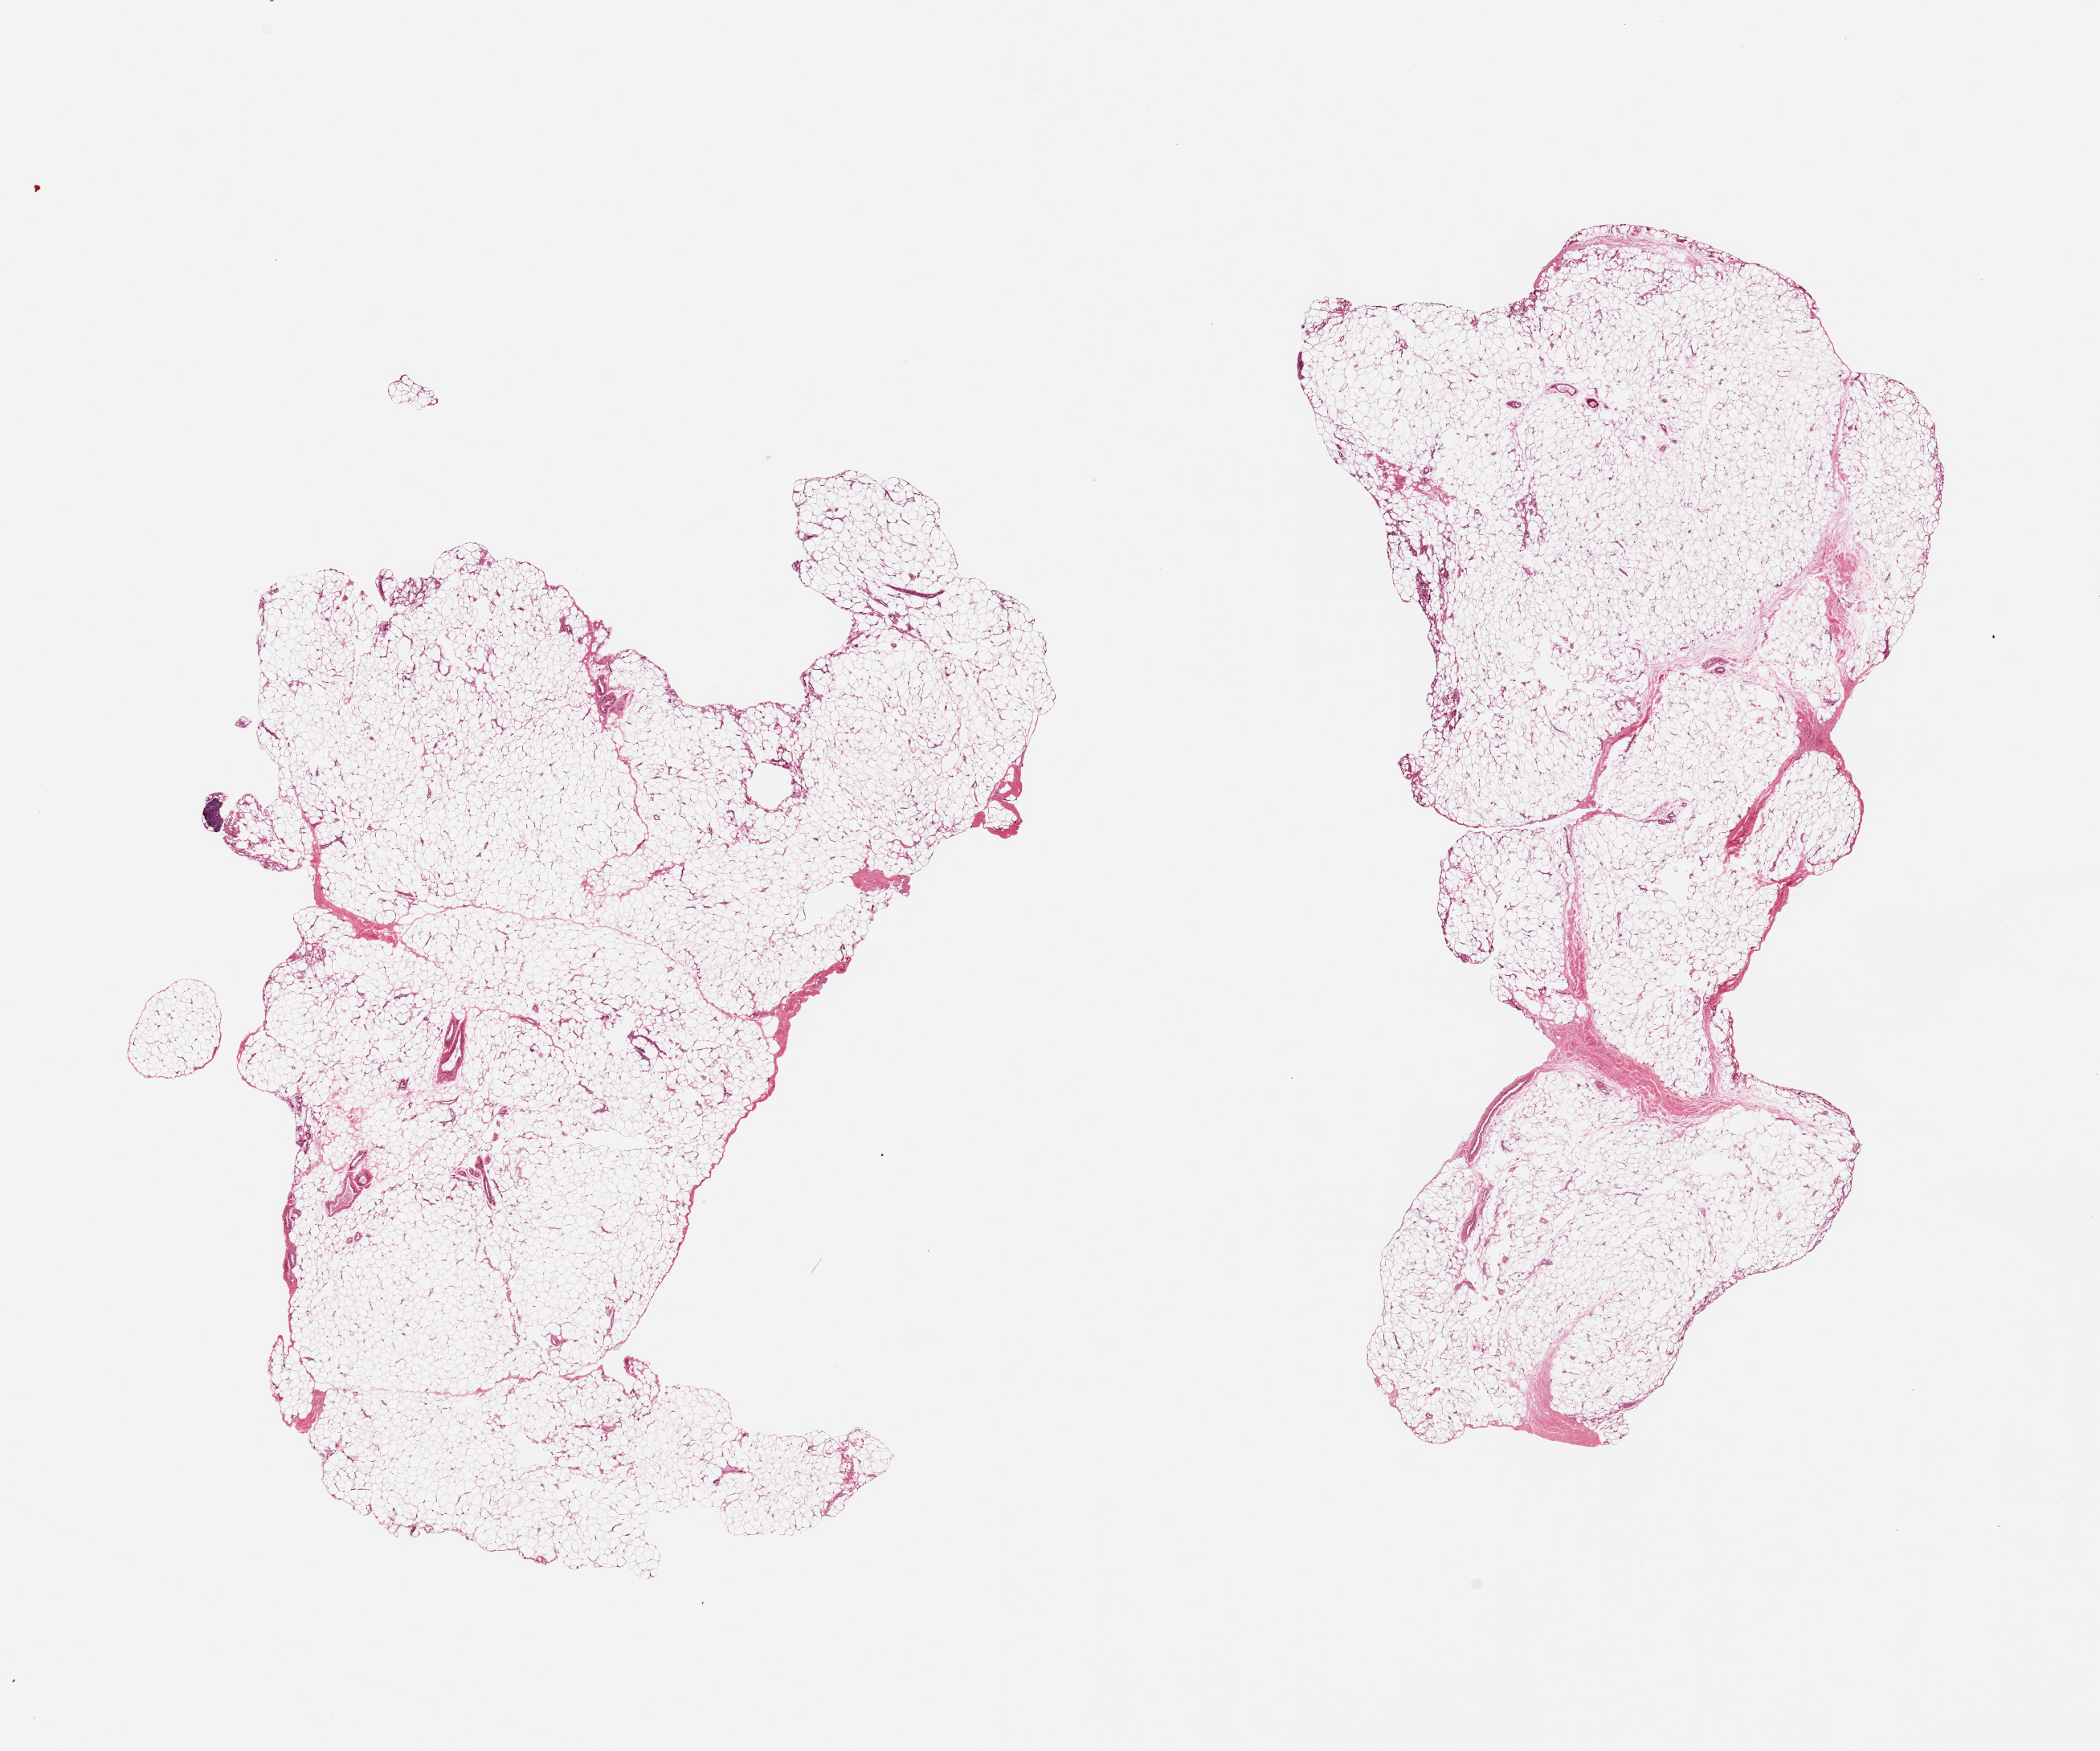
Whole-slide image, hematoxylin and eosin (H&E) stain, brightfield, a low-resolution overview of the entire scanned area, about 20.7 x 17.2 mm (from a 20x scan), PAXgene-fixed, paraffin-embedded tissue, section of adipose tissue (target tissue), donor tissue sample. Female donor.
* review note (as recorded): 2 pieces; small squamous carry-over artifact